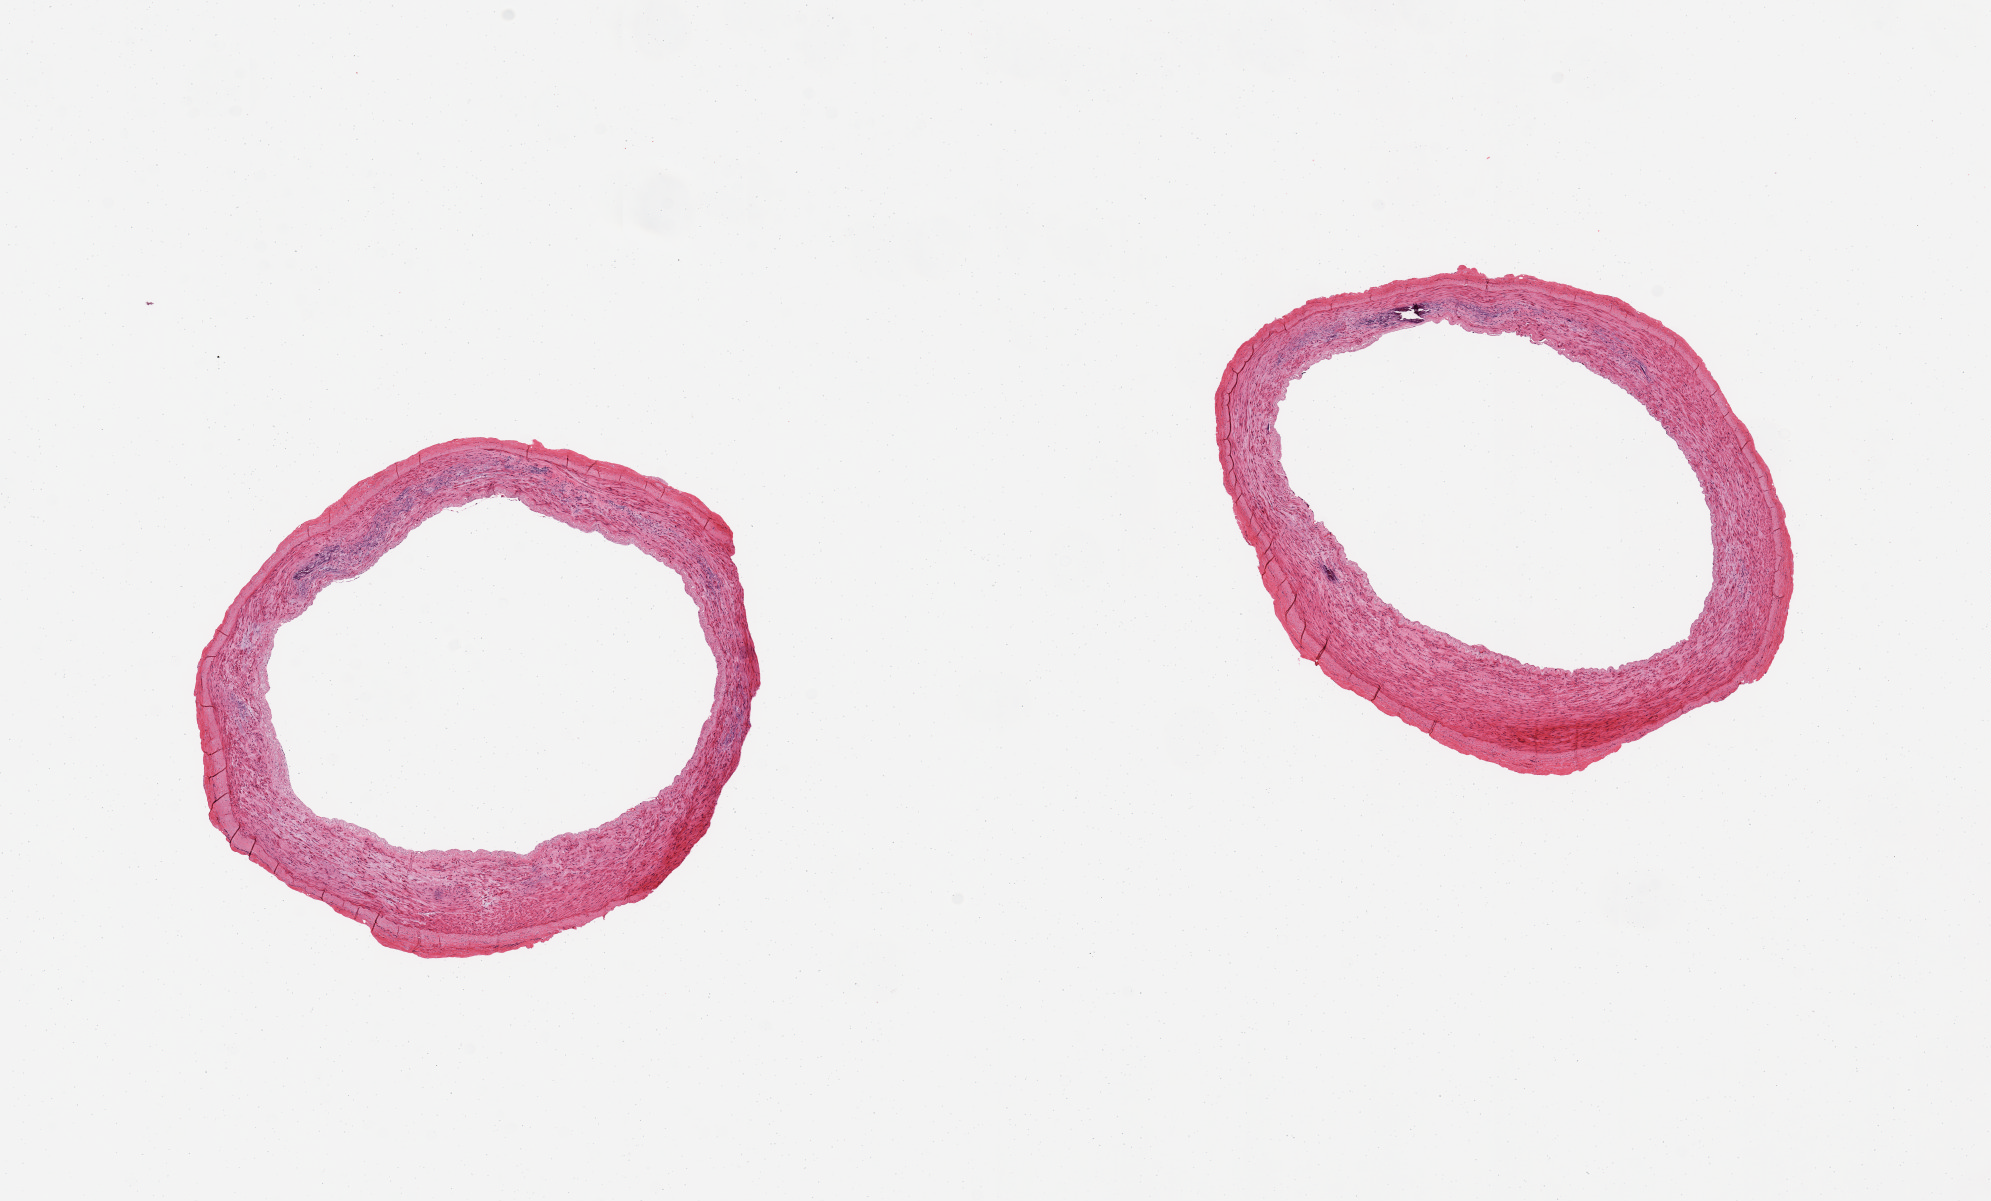
H&E whole-slide image, brightfield — whole scanned area (about 15.8 x 9.5 mm) shown as a low-resolution overview; PAXgene-fixed paraffin-embedded (PFPE) section; section of tibial artery (target tissue); donor tissue sample. Donor sex: female.
Review note (as recorded): 2 pieces, medial cacific sclerosis (Monckeberg's arteriosclerosis), well trimmed.